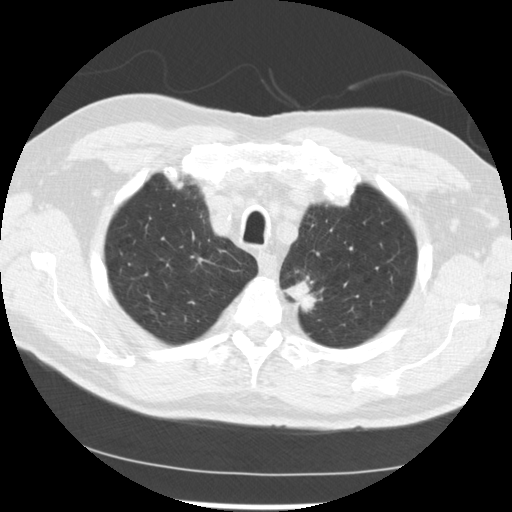
Low-dose screening chest CT, one axial slice. Slice 208 of 249 in the series (ordered by position). 120 kVp. Lung window (W 1500 / L -600 HU). 2.5 mm slice thickness. 512 × 512 image matrix, field of view 341 × 341 mm.
Outlined on this slice (outlined manually by an expert reader):
- lesion 2 (tumor, upper lobe of left lung): box from (x=286, y=280) to (x=317, y=312) px